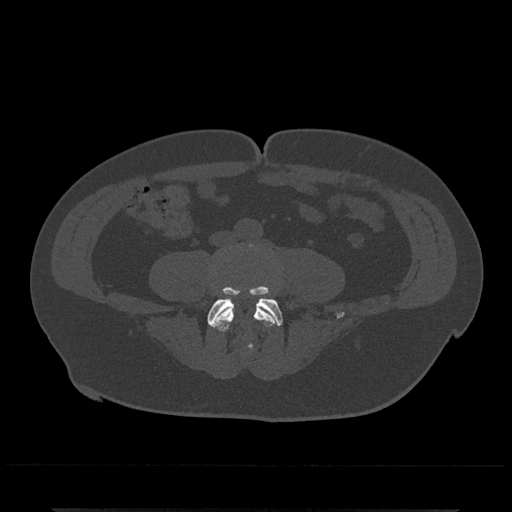
CT including the spine, one axial slice. Slice 118 of 797 in the series (ordered by position). Reconstruction kernel Br40s/3. Bone window (W 1800 / L 400 HU). 512 × 512 image matrix, field of view 393 × 393 mm. Male patient, age 67 years. Case-level facts recorded for this patient, not image findings: primary cancer: prostate.
Outlined on this slice (semi-automatically segmented with operator editing):
- L4 vertebra: bounding box [x1, y1, x2, y2] px = [212, 302, 280, 349]
- L5 vertebra: [207, 286, 283, 326]